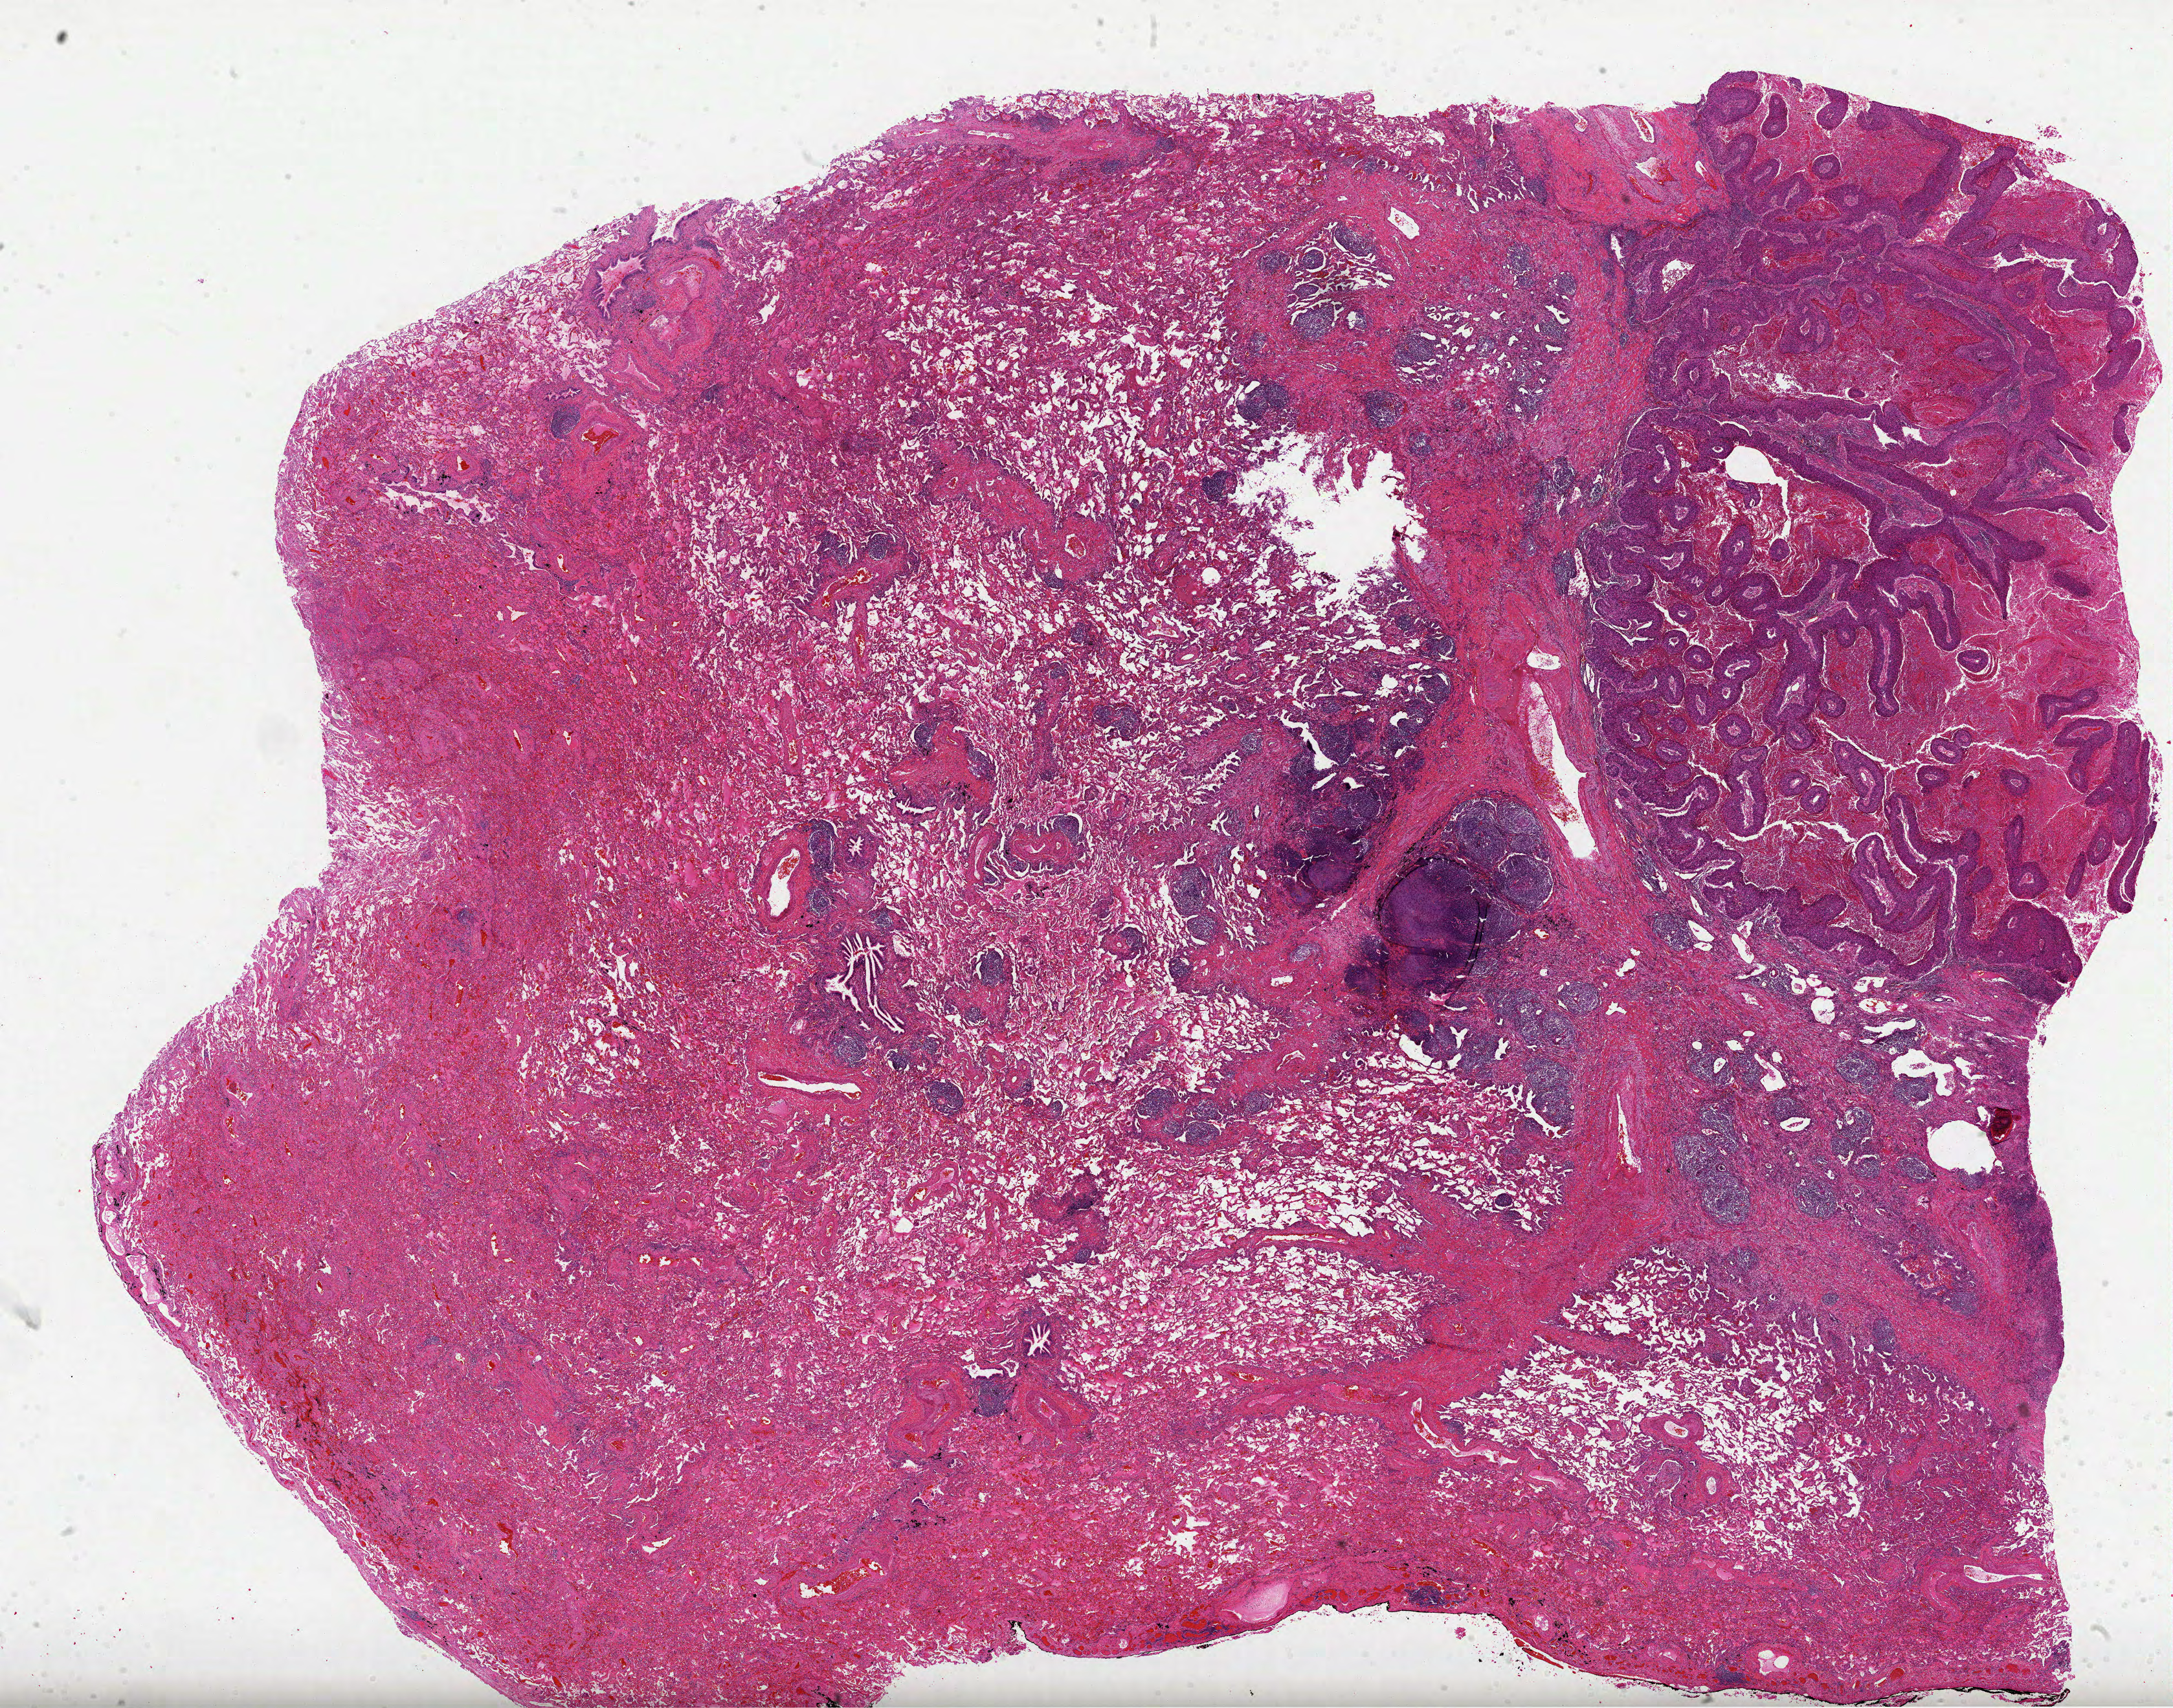
Hematoxylin and eosin (H&E) stained whole-slide image, shown as a low-resolution overview of the whole scanned area (about 27.1 x 21.3 mm). Formalin-fixed paraffin-embedded (FFPE) diagnostic section. Primary tumour sample from the lung. Male patient; age at initial diagnosis 73 years.
* AJCC pathologic stage: IA (5th edition)
* TNM: T1 N0 M0
* diagnosis: Squamous cell carcinoma, NOS (lower lobe, lung)